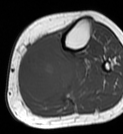
MRI of an extremity soft-tissue mass, one axial slice. Position 30 of 68 along the scan axis. MR volume resampled by the dataset authors to the PET/CT grid (not the native acquisition matrix). 3.27 mm slice thickness. 123 × 134 image matrix. Female patient. Case-level facts recorded for this patient, not image findings: histological type: extraskeletal high grade osteogenic sarcoma; grade: high; site of the primary tumour: left calf.
Structures marked on this image (expert contour drawn on MRI and transferred to this co-registered scan by the dataset authors):
- gross tumour volume (mass): bounding box (x1, y1, x2, y2) in pixels: (20, 36, 75, 104)